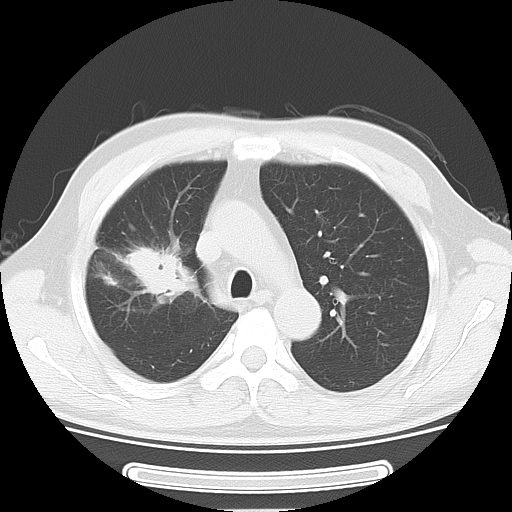
Chest CT, one axial slice; slice 37 of 51 in the series (ordered by position); reconstruction kernel LUNG; lung window (W 1500 / L -600 HU); 5 mm slice thickness; 512 × 512 image matrix. Male patient, age 46 years. Case-level facts recorded for this patient, not image findings: clinical TNM (as recorded): T3 N0 M1b.
Outlined on this slice (bounding box drawn by a radiologist):
- lung tumour (recorded histology: adenocarcinoma): bounding box [x1, y1, x2, y2] px = [107, 230, 191, 314]